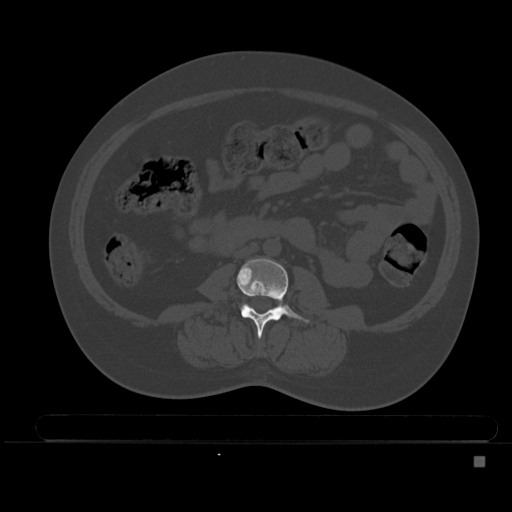
CT including the spine, one axial slice; position 149 of 495 along the scan axis; bone window (W 1800 / L 400 HU); 512 × 512 image matrix, field of view 404 × 404 mm. Patient: female, 33 years. From the clinical record (not read from this slice): primary cancer: breast; vertebrae with lytic lesions (as recorded): T1.
Structures marked on this image (semi-automatically segmented with operator editing):
- L3 vertebra: box from (x=237, y=259) to (x=311, y=337) px